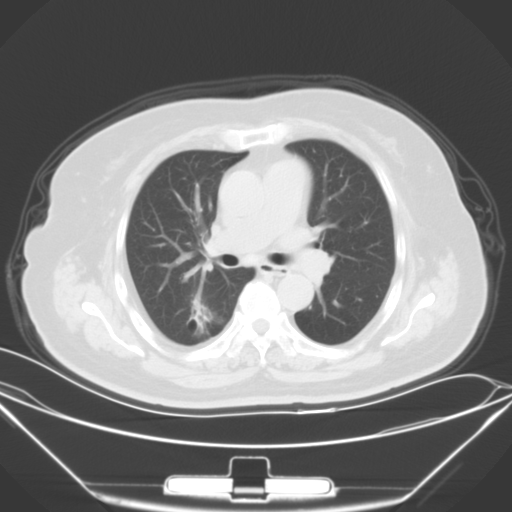
Chest CT, one axial slice; position 38 of 64 along the scan axis; lung window (W 1500 / L -600 HU); 5 mm slice thickness; 512 × 512 image matrix. Patient: female, 70 years. Case-level facts recorded for this patient, not image findings: clinical TNM (as recorded): T2 N0 M3.
Structures marked on this image (bounding box drawn by a radiologist):
- lung tumour (recorded histology: adenocarcinoma): bounding box <169,291,230,342> (left, top, right, bottom; pixels)